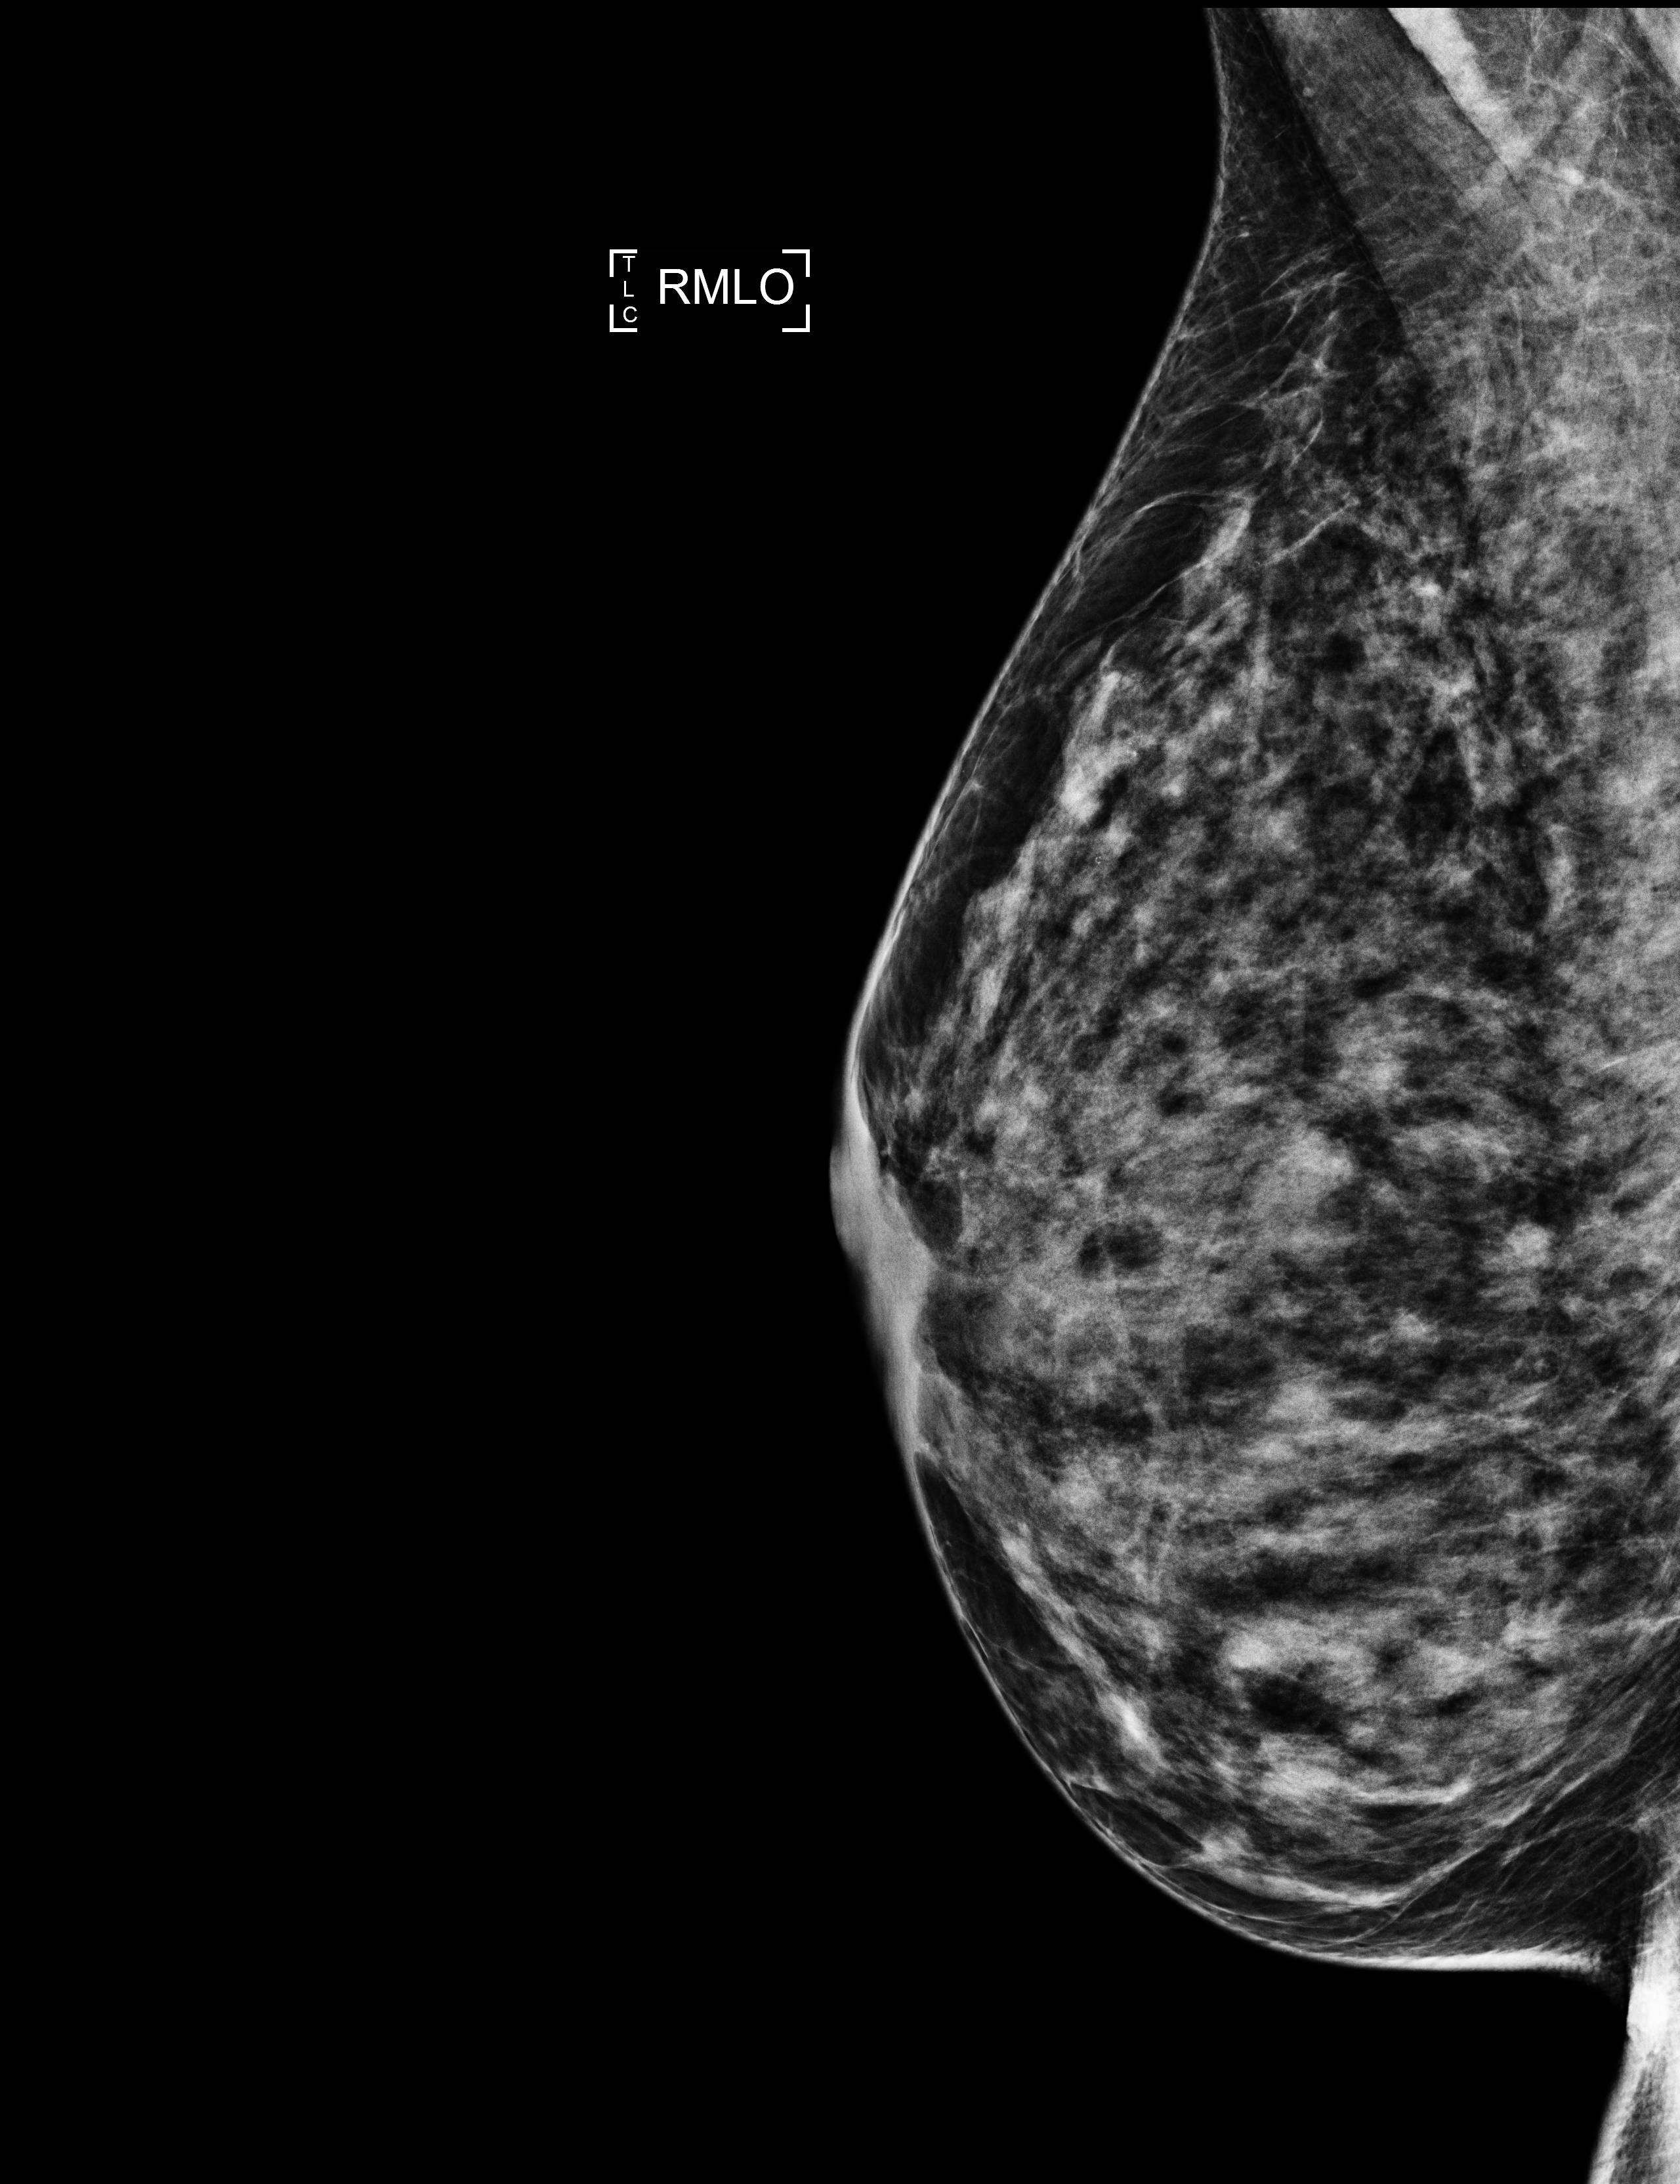
Screening examination. Patient aged 53 years (female).
Image type: full-field digital mammogram. Breast: right. Projection: medio-lateral oblique projection.